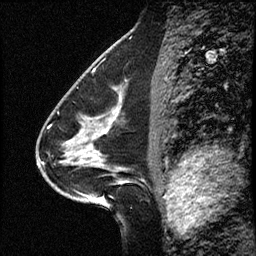
Breast MRI (dynamic contrast-enhanced), one sagittal slice. Slice 29 of 50 in the series (ordered by position). Dynamic contrast-enhanced study with each time point stored as its own series, time point 2 of 4 at this slice position (early post-contrast, ordered by acquisition time). 1.5 T. TE 4.2 ms, TR 17.5 ms. 256 × 256 image matrix, field of view 200 × 200 mm. From the clinical record (not read from this slice): setting: breast cancer imaged before/during neoadjuvant chemotherapy.
Structures marked on this image (semi-automatic segmentation, software-assisted and operator-edited):
- analysis volume of interest (the breast-tissue region the enhancement analysis was run in; not a lesion): box from (x=52, y=98) to (x=157, y=207) px
- tumour enhancement mask (voxels above the 100 % enhancement threshold inside the analysis volume of interest): (x=80, y=99)–(x=120, y=162)